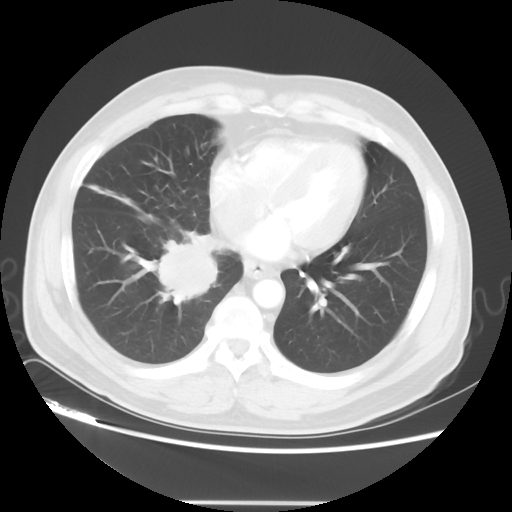
Chest CT, one axial slice; position 16 of 48 along the scan axis; lung window (W 1500 / L -600 HU); 5 mm slice thickness; 512 × 512 image matrix. Patient: male, 53 years. From the clinical record (not read from this slice): clinical TNM (as recorded): T2 N3 M0; histopathological grade: G3.
Outlined on this slice (bounding box drawn by a radiologist):
- lung tumour (recorded histology: small cell carcinoma): bounding box <148,230,223,309> (left, top, right, bottom; pixels)